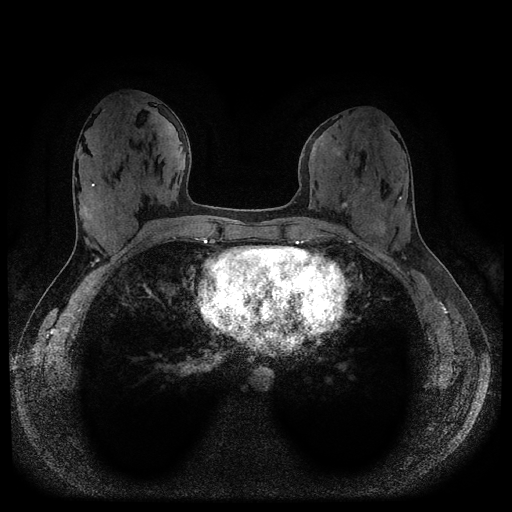
Breast MRI (dynamic contrast-enhanced, multi-phase), one axial slice; slice 43 of 116 in the series (ordered by position); dynamic contrast-enhanced series, time point 2 of 5 at this slice position (early post-contrast); 1.5 T; TE 2.6 ms, TR 5.3 ms; 2 mm slice thickness; 512 × 512 image matrix, field of view 350 × 350 mm. Patient: female, 33 years.
Annotated regions visible in this slice (semi-automatically segmented with operator editing):
- breast lesion (labelled benign in the annotation): bounding box <339,199,349,209> (left, top, right, bottom; pixels)